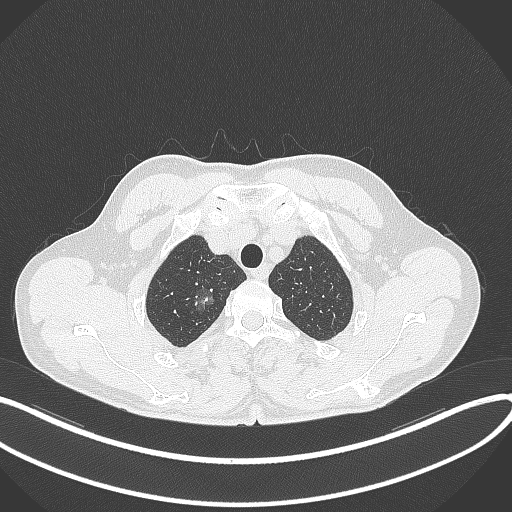
Chest CT, one axial slice. Position 332 of 407 along the scan axis. Reconstruction kernel B70f. 120 kVp. Lung window (W 1500 / L -600 HU). 512 × 512 image matrix, field of view 400 × 400 mm. Male patient, age 58 years. Case-level facts recorded for this patient, not image findings: clinical TNM (as recorded): T1c N0 M0.
Structures marked on this image (rectangle marked by the reading radiologist):
- lung tumour (recorded histology: adenocarcinoma): box from (x=179, y=279) to (x=221, y=319) px